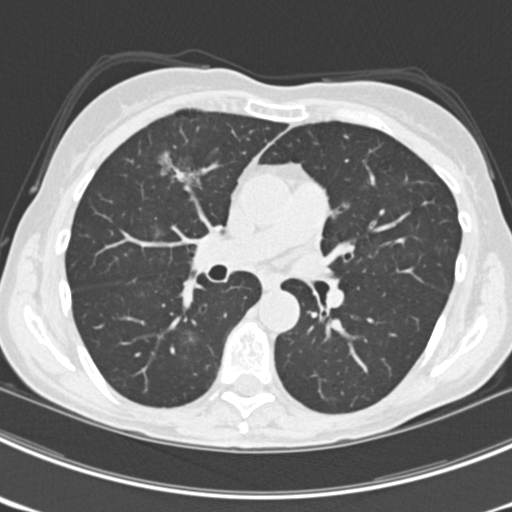
Chest CT (low-dose screening protocol), one axial image, third annual screen, lung window (W 1500 / L -600 HU), standard (soft-tissue) reconstruction kernel (B30f), slice 92 of 225 in the series, 512 × 512 image matrix, field of view 302 × 302 mm. Female participant, aged 63 years at enrolment.
Expert-annotated lung lesion, bounding box (x1, y1, x2, y2) in pixels: (151, 141, 216, 200). The screening reader recorded 9 non-calcified nodules or masses ≥4 mm on this exam; which of them this box marks is not recorded. Official screen result: positive, other. Later outcome: lung cancer diagnosed 15 days after this screen — bronchiolo-alveolar adenocarcinoma, NOS, right upper lobe, right middle lobe, right lower lobe, left upper lobe, left lower lobe, moderately differentiated (G2), stage IV (AJCC 6th edition).